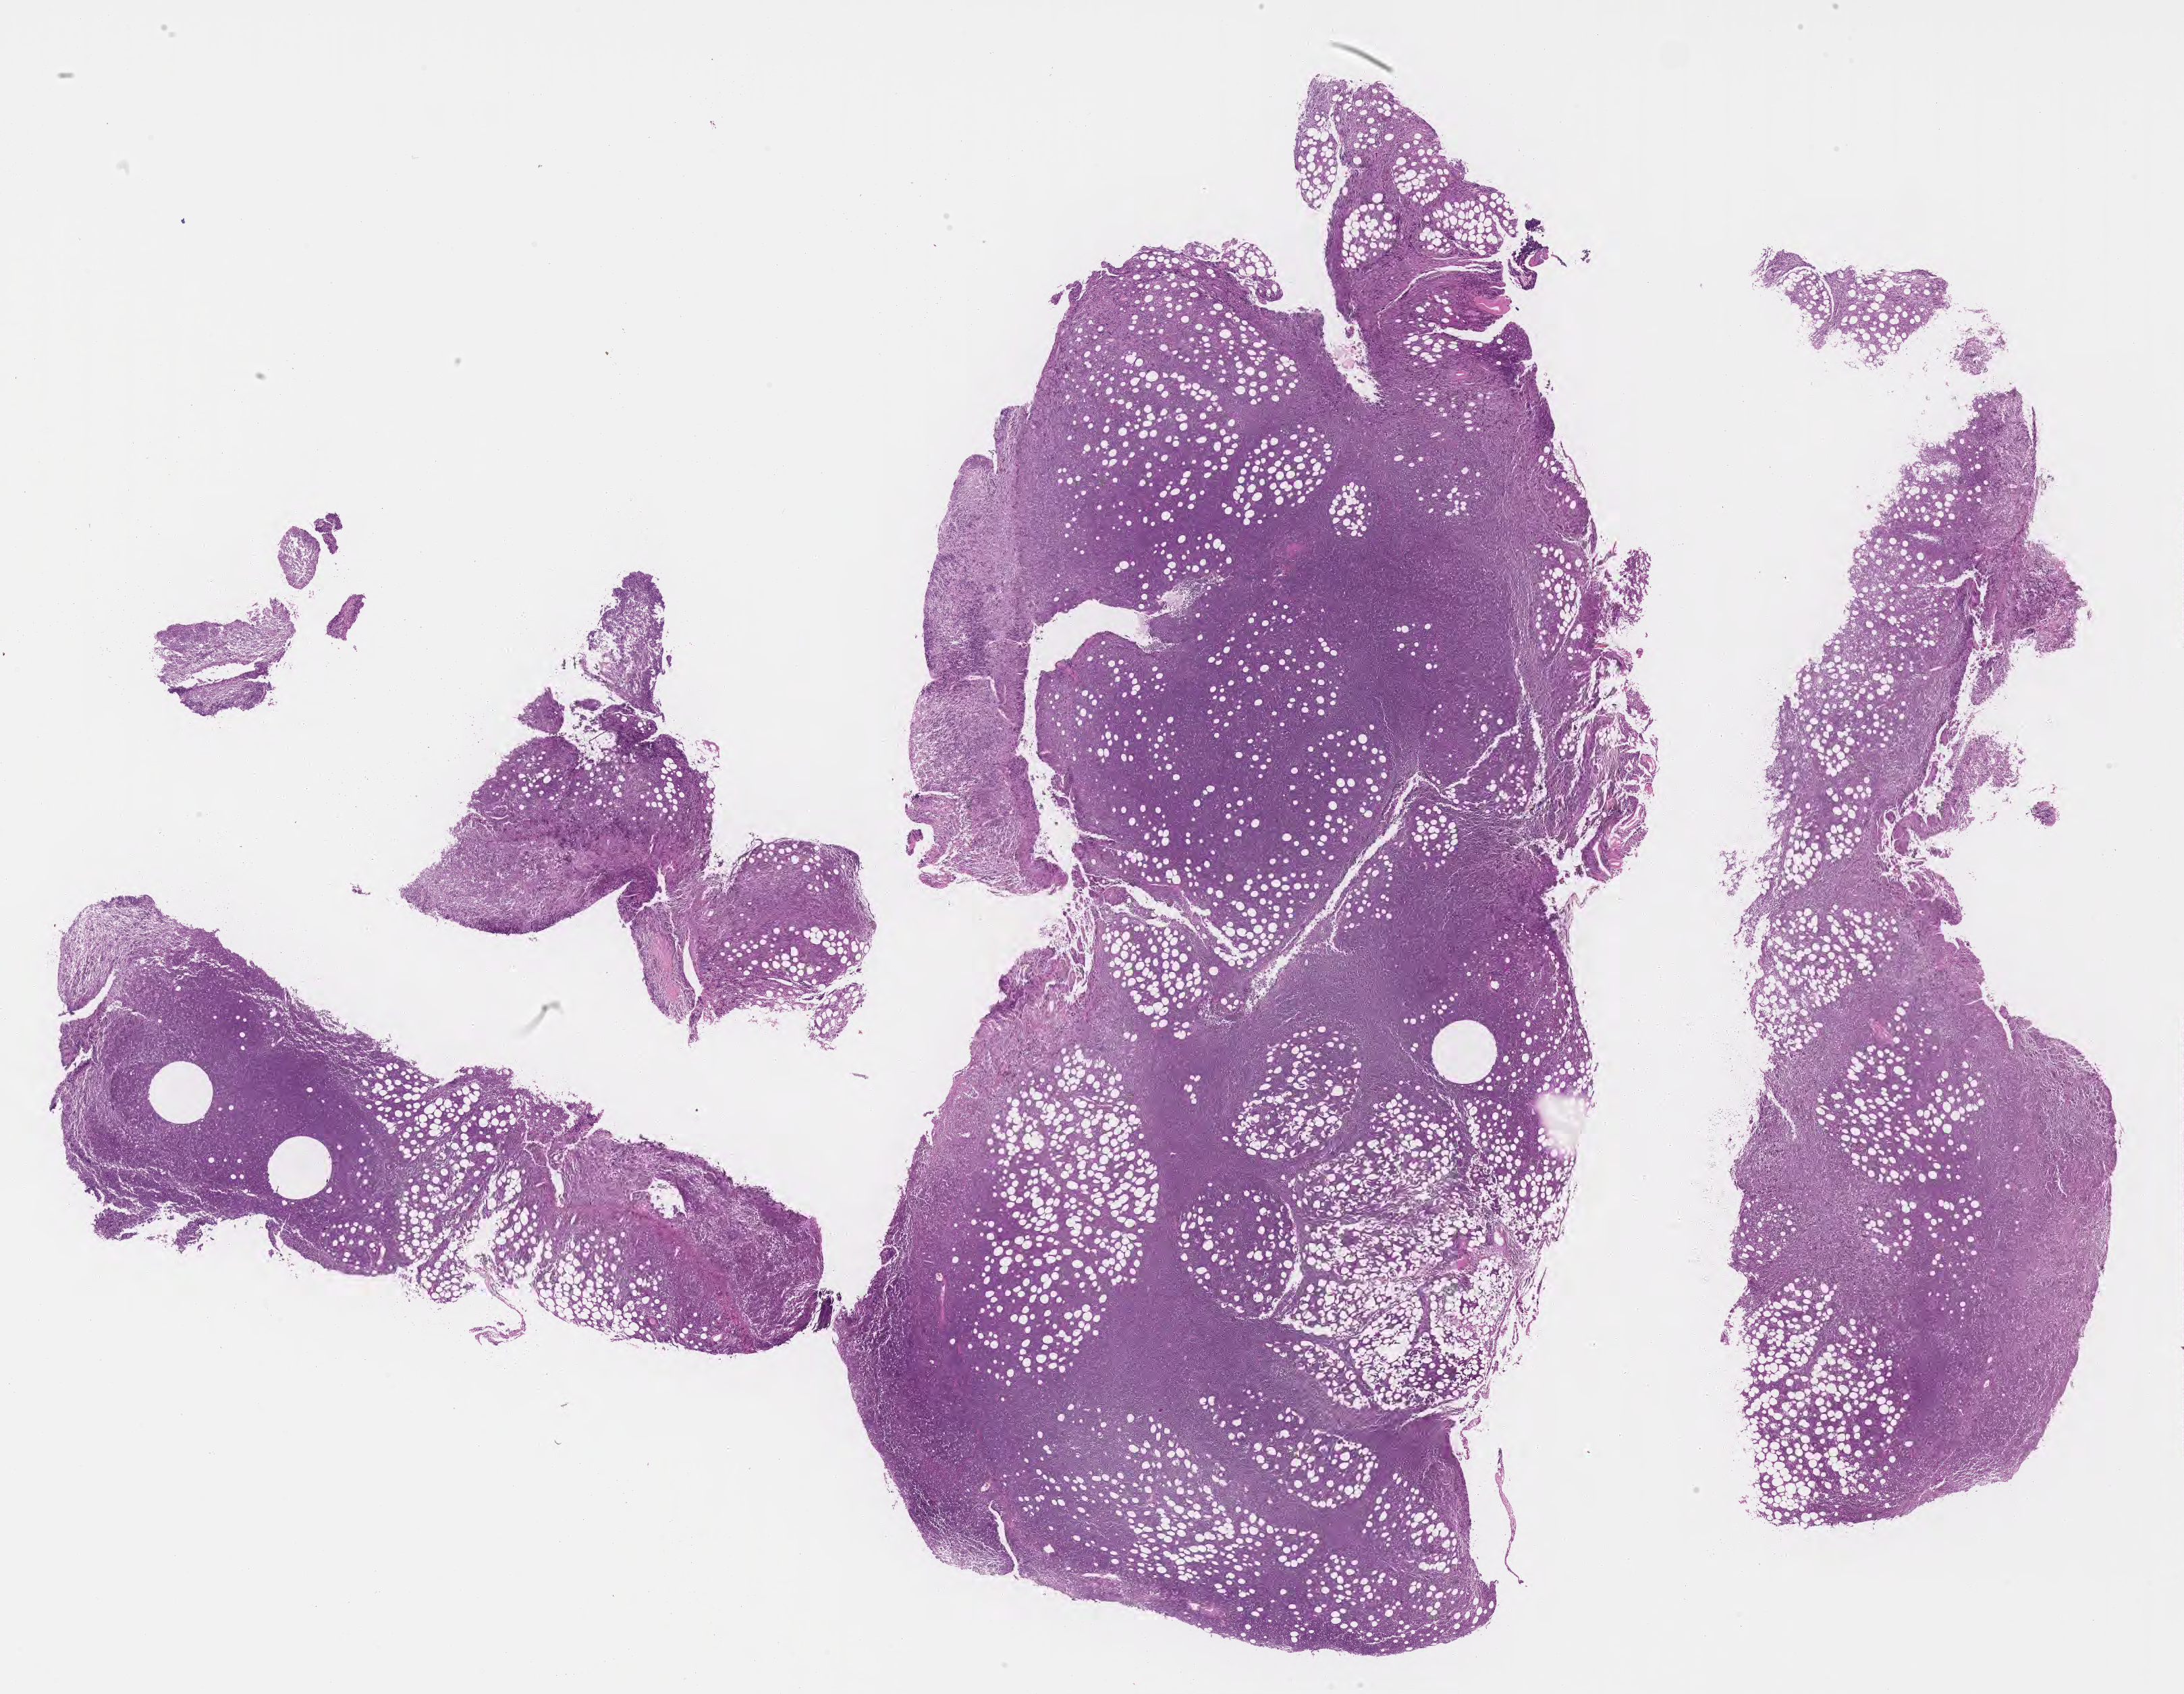
Digitized haematoxylin and eosin-stained section, low-resolution overview of the scanned area, about 26.2 x 20.3 mm, formalin-fixed, paraffin-embedded (FFPE) tissue, primary tumor. Patient: male, aged 31. Slide review estimates, as recorded: tumor cells 85%, tumor nuclei 95%, stromal cells 10%, necrosis 5%, normal cells 0%. Inflammatory infiltration, as recorded: lymphocyte infiltration 40%, monocyte infiltration 30%, neutrophil infiltration 5%.
- Ann Arbor stage (patient): Stage IV
- diagnosis: Burkitt lymphoma, NOS